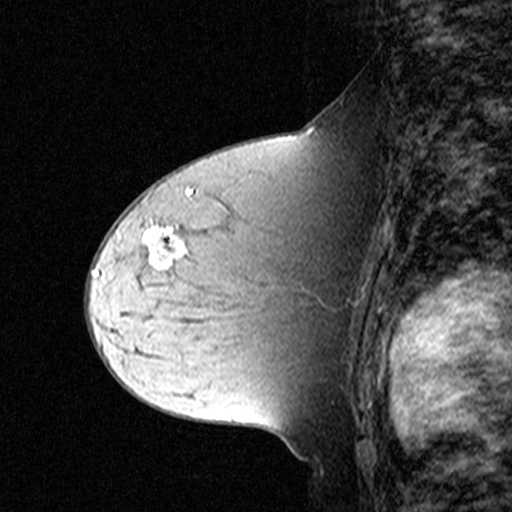
Breast MRI (dynamic contrast-enhanced), one sagittal slice. Slice 25 of 44 in the series (ordered by position). Dynamic contrast-enhanced study with each time point stored as its own series, time point 2 of 3 at this slice position (early post-contrast, ordered by acquisition time). 1.5 T. TE 4.5 ms, TR 11 ms. 3 mm slice thickness. 512 × 512 image matrix. Patient: female, 44 years. From the clinical record (not read from this slice): setting: breast cancer imaged before/during neoadjuvant chemotherapy; receptor status: triple-negative.
Annotated regions visible in this slice (semi-automatic segmentation, software-assisted and operator-edited):
- analysis volume of interest (the breast-tissue region the enhancement analysis was run in; not a lesion): box from (x=132, y=212) to (x=309, y=331) px
- tumour enhancement mask (voxels above the 90 % enhancement threshold inside the analysis volume of interest): (x=147, y=227)–(x=188, y=269)